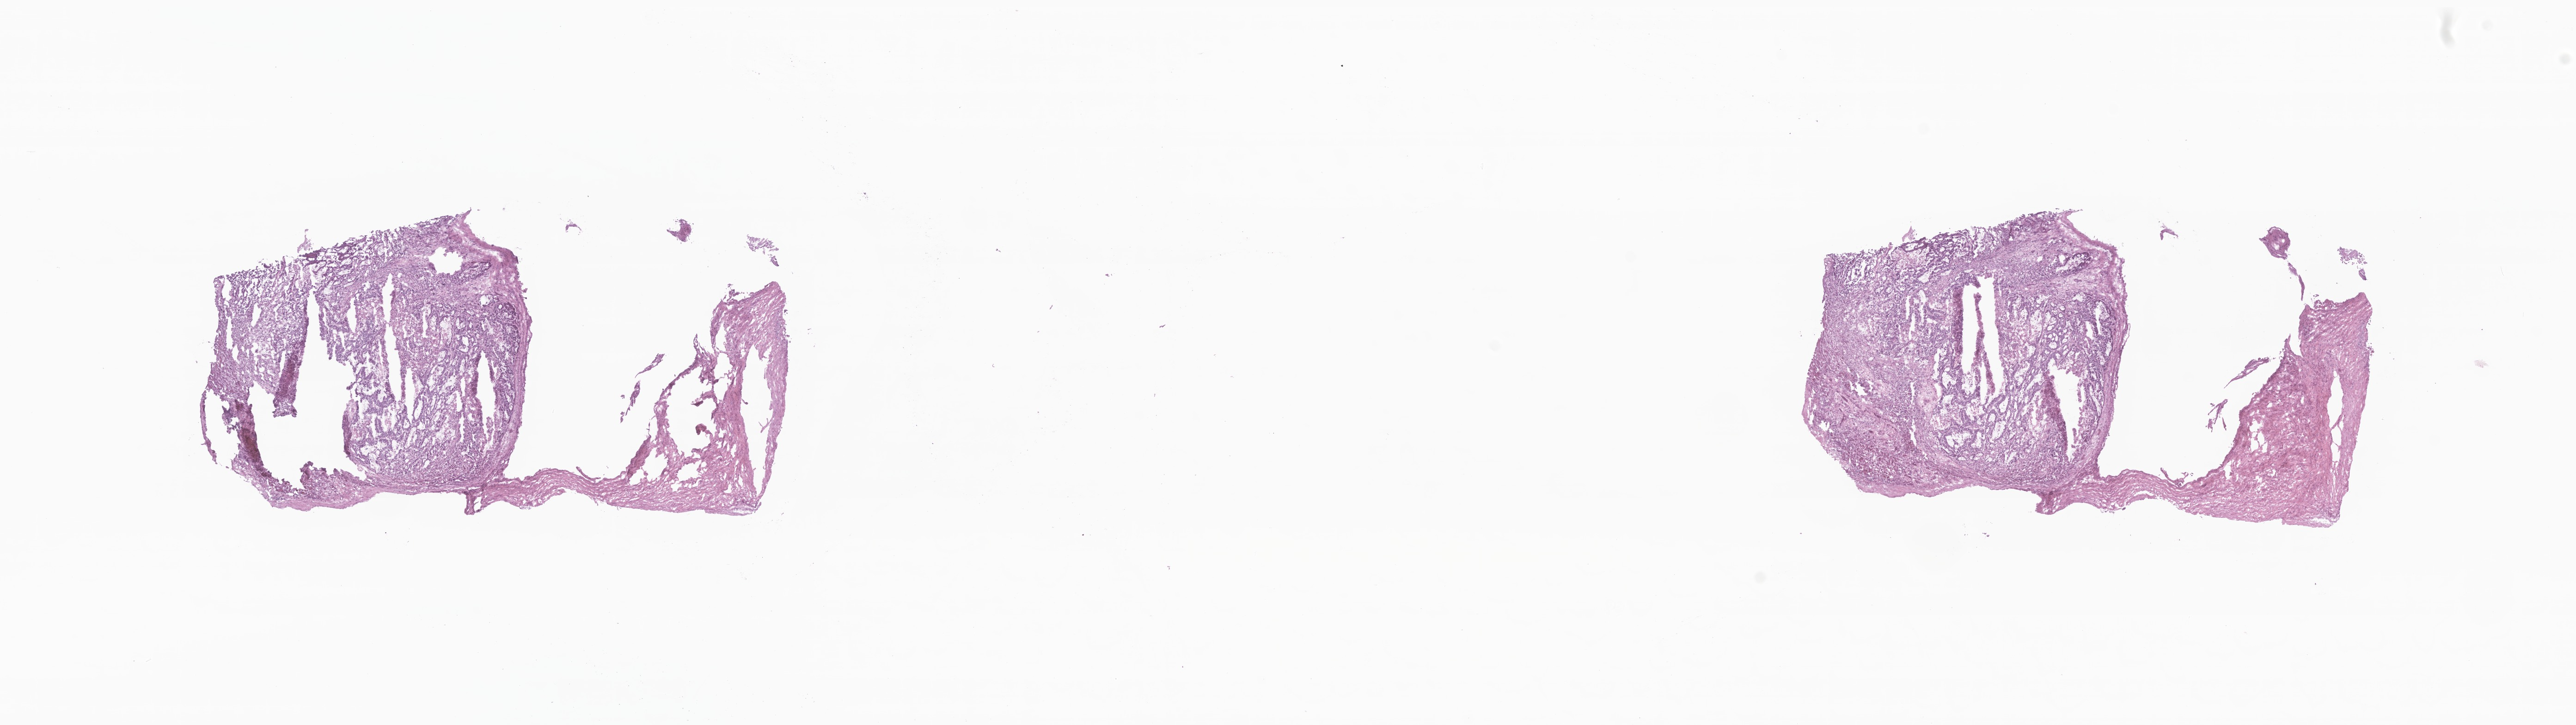
Whole-slide image, haematoxylin and eosin stain — shown as a low-resolution overview of the whole scanned area (about 23.5 x 6.6 mm). Cryosection. Metastatic tumor tissue, resected from liver. Male patient; age at initial diagnosis 72 years. Slide review estimates, as recorded: tumor cells 80%, tumor nuclei 80%.
Patient diagnosis (primary): Adenocarcinoma, NOS.